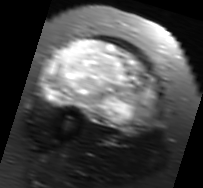
MRI of an extremity soft-tissue mass, one axial slice; slice 36 of 91 in the series (ordered by position); T2-weighted fat-saturated; MR volume resampled by the dataset authors to the PET/CT grid (not the native acquisition matrix); 3.27 mm slice thickness; 203 × 188 image matrix, field of view 198 × 184 mm. Female patient. Case-level facts recorded for this patient, not image findings: histological type: malignant solitary fibrous tumor; grade: intermediate; site of the primary tumour: right thigh.
Outlined on this slice (expert contour drawn on MRI and transferred to this co-registered scan by the dataset authors):
- gross tumour volume including surrounding oedema: box from (x=38, y=38) to (x=160, y=132) px
- gross tumour volume (mass): (x=44, y=38)–(x=157, y=128)